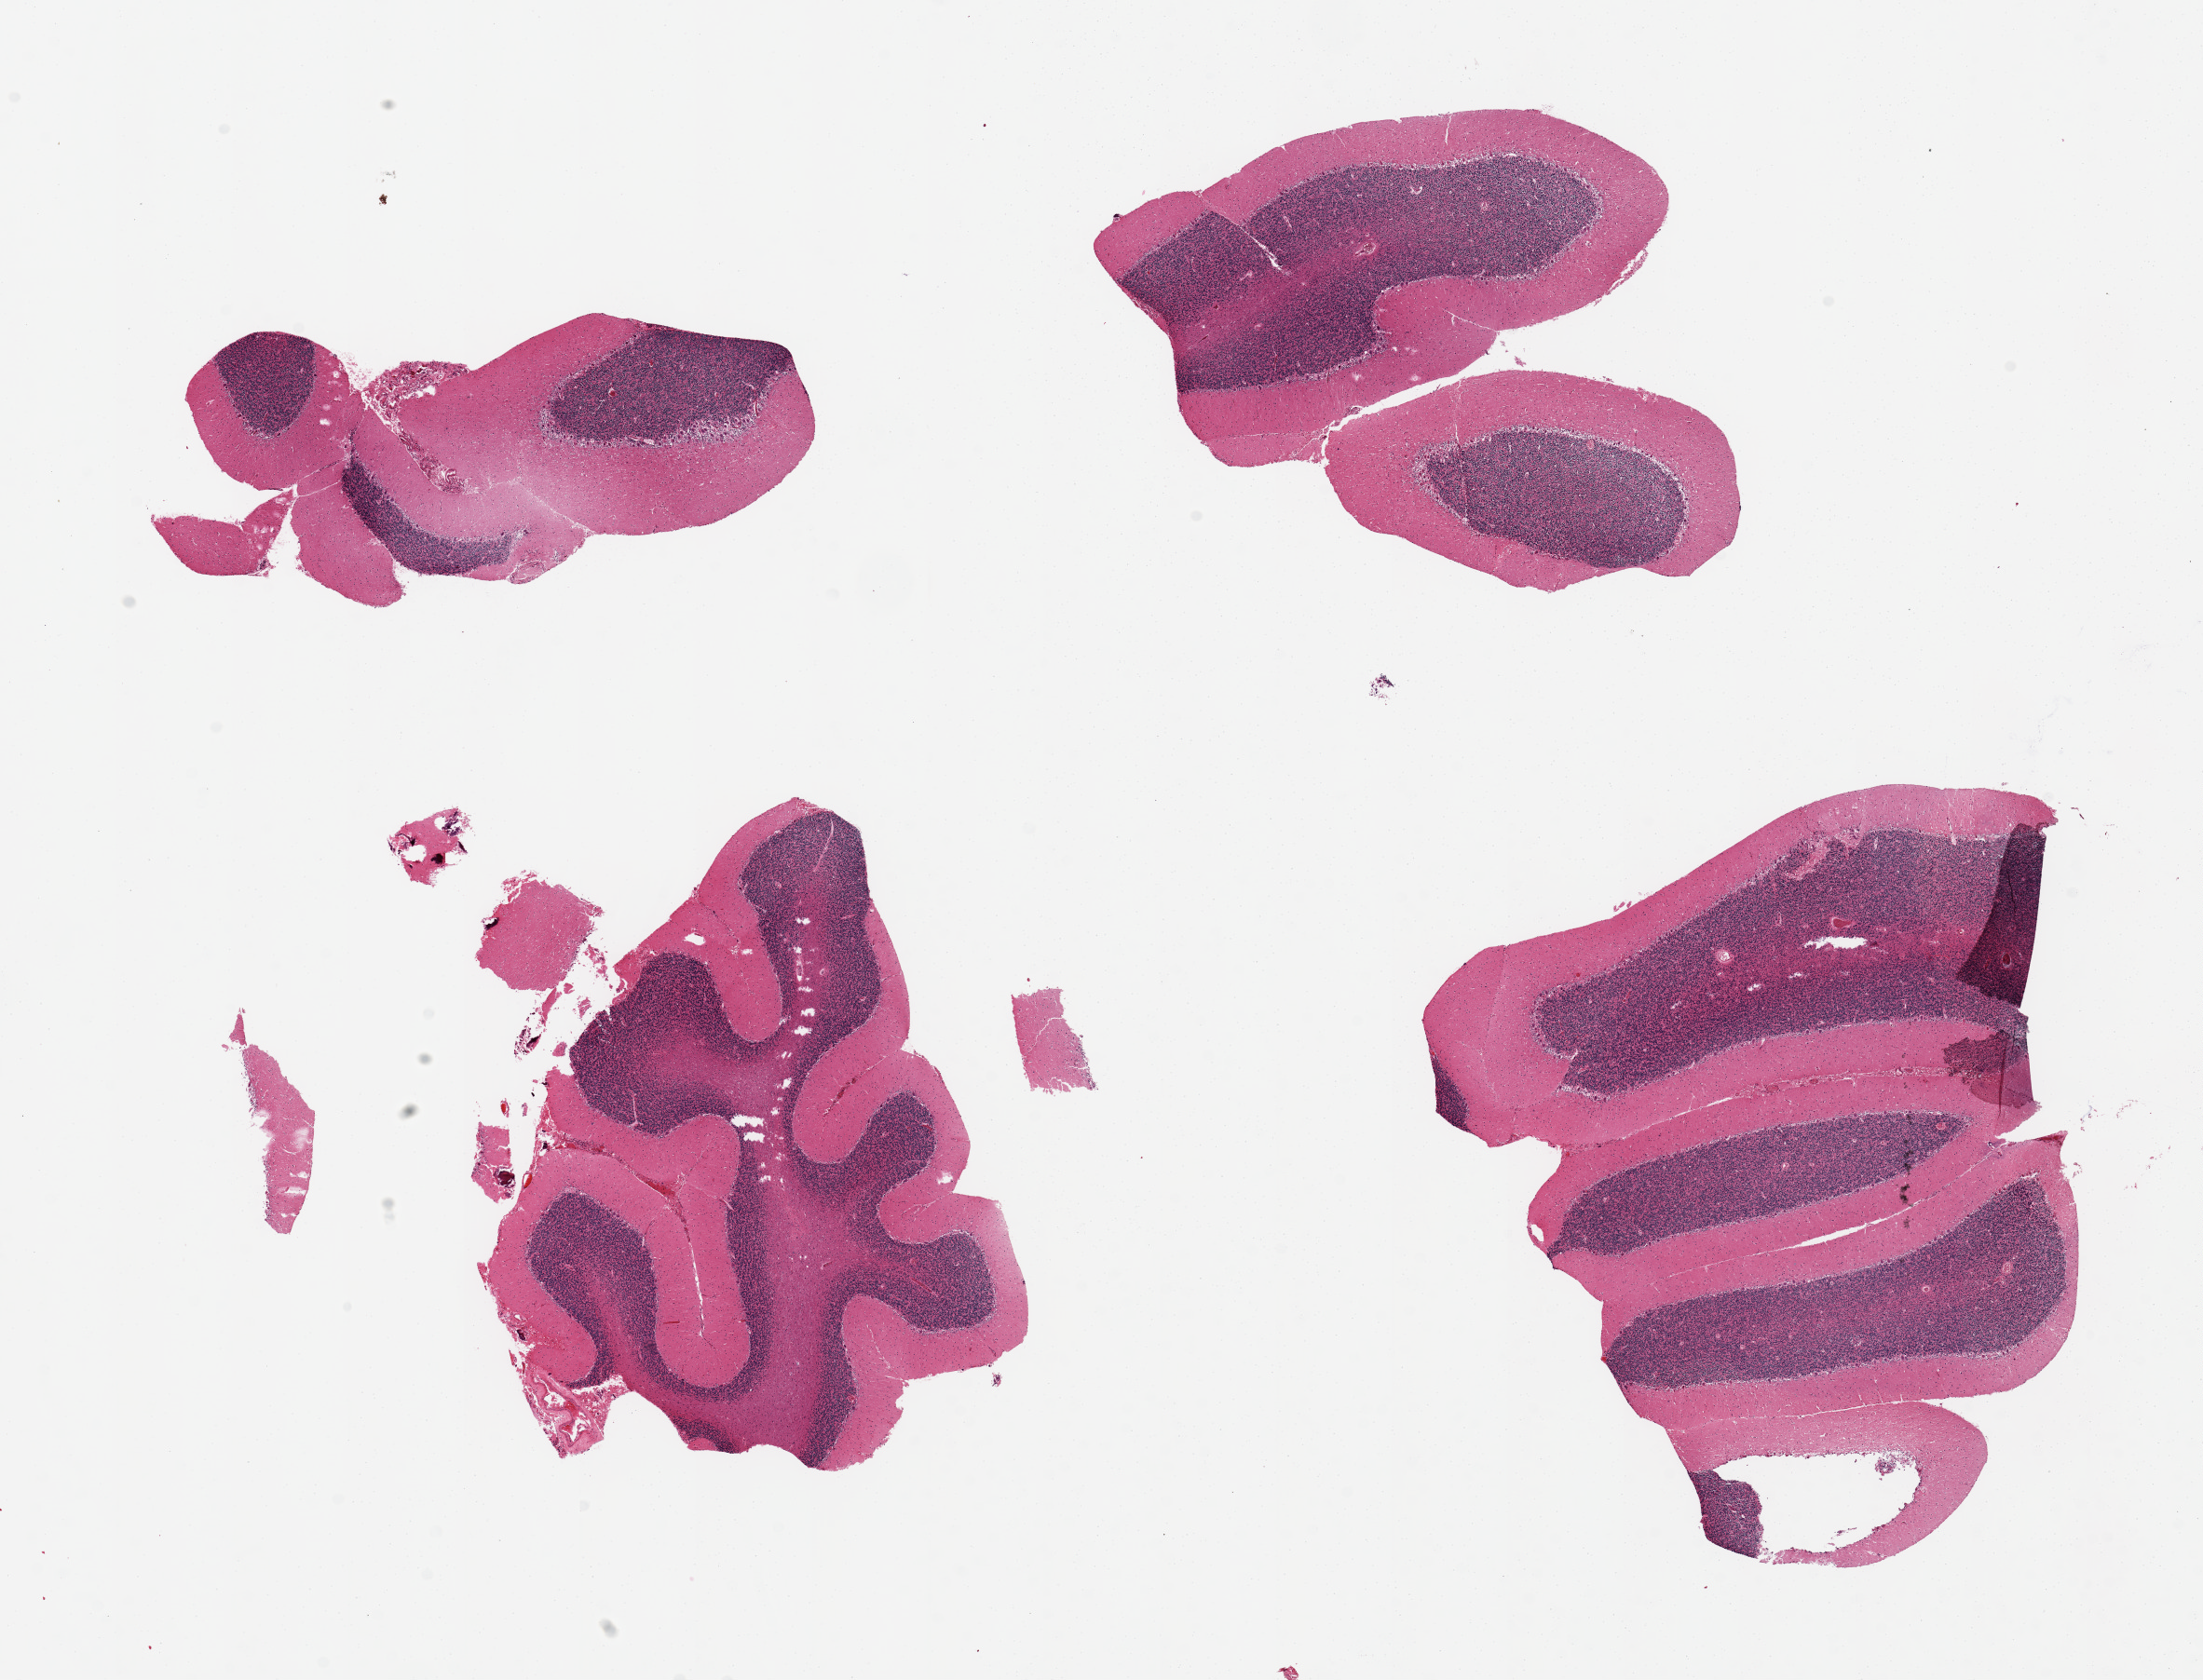
Digitized H&E-stained section, whole scanned area (about 18.7 x 14.3 mm, slide scanned at 20x) shown as a low-resolution overview. PAXgene-fixed, paraffin-embedded tissue. Sampled site (target tissue): cerebellum. Tissue donor sample.
Pathologist's review note for this sample: 4 ~6x4 fragmented aliquots.